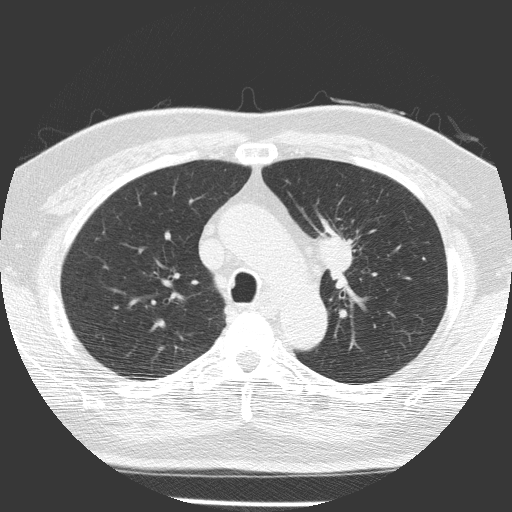
Low-dose screening chest CT, one axial slice. Position 109 of 156 along the scan axis. Reconstruction kernel FC51. 120 kVp. Lung window (W 1500 / L -600 HU). 512 × 512 image matrix, field of view 309 × 309 mm.
Outlined on this slice (expert manual segmentation):
- lesion 1 (tumor, upper lobe of left lung): bounding box (x1, y1, x2, y2) in pixels: (319, 231, 354, 279)